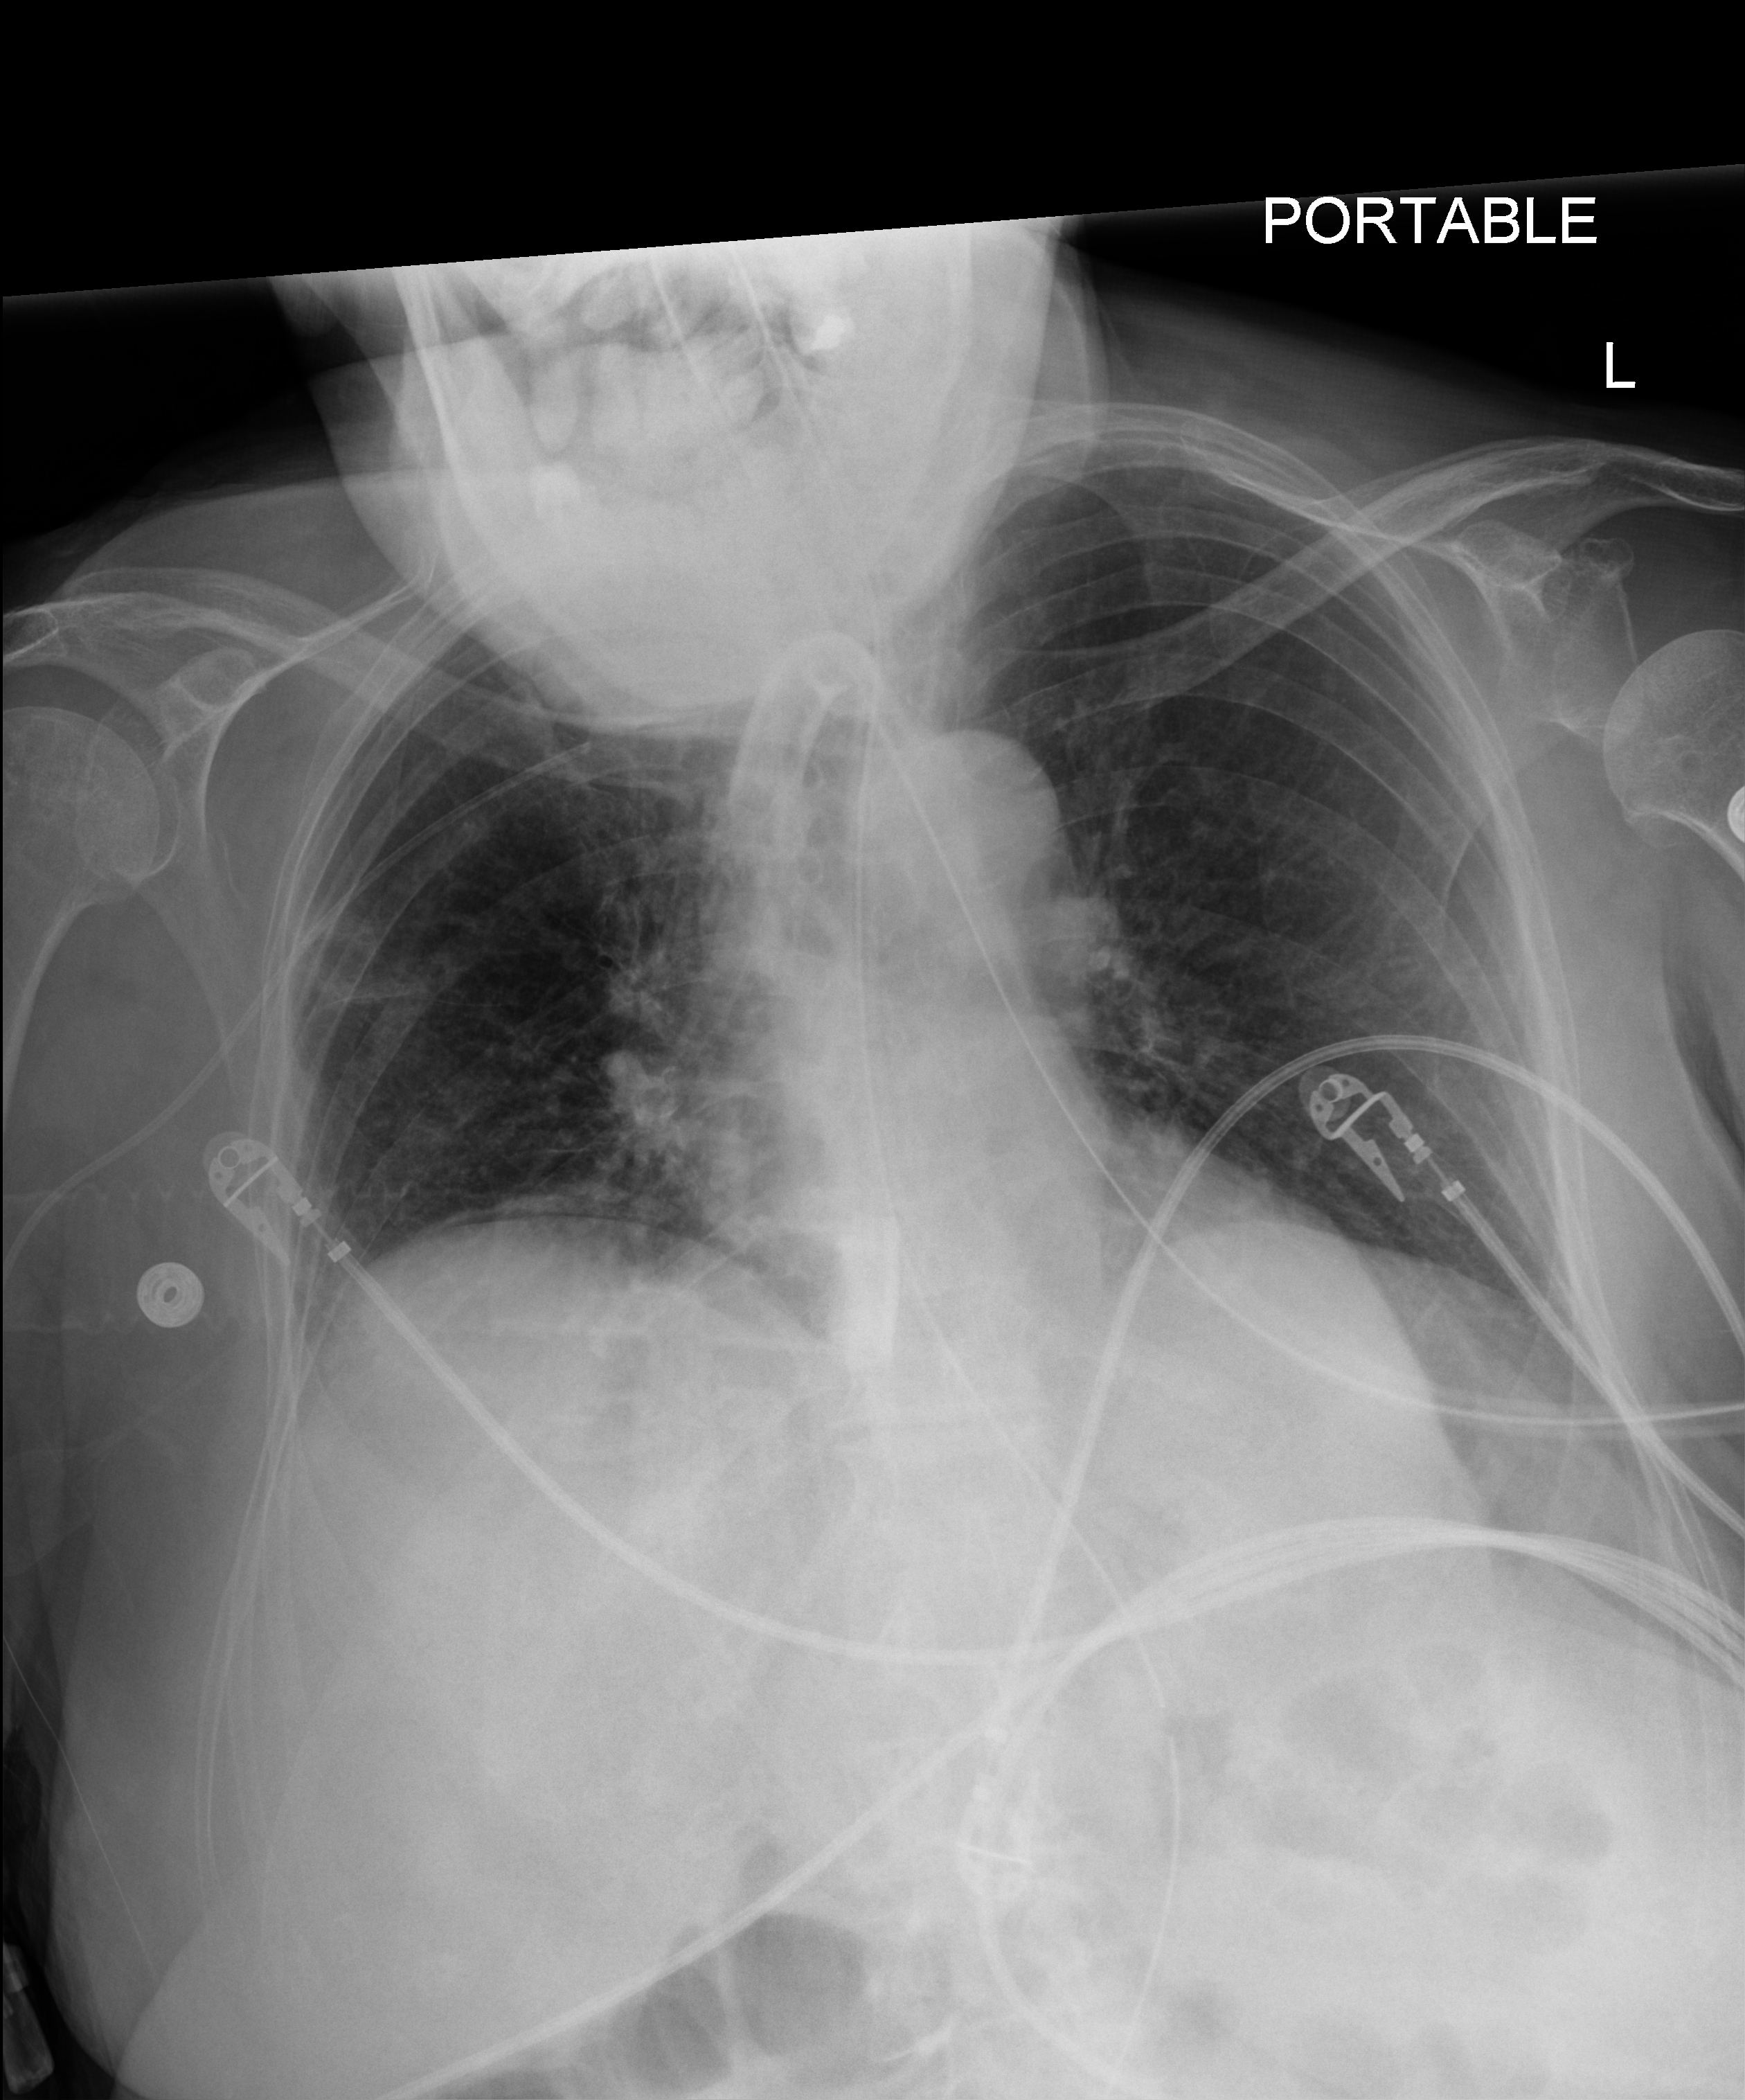
Chest radiograph (digital radiography). Female patient hospitalised with COVID-19, age 75–90 years.
Admission-level facts for this patient (not findings on this image; timing relative to this image not recorded): mechanically ventilated during this hospital stay: yes.